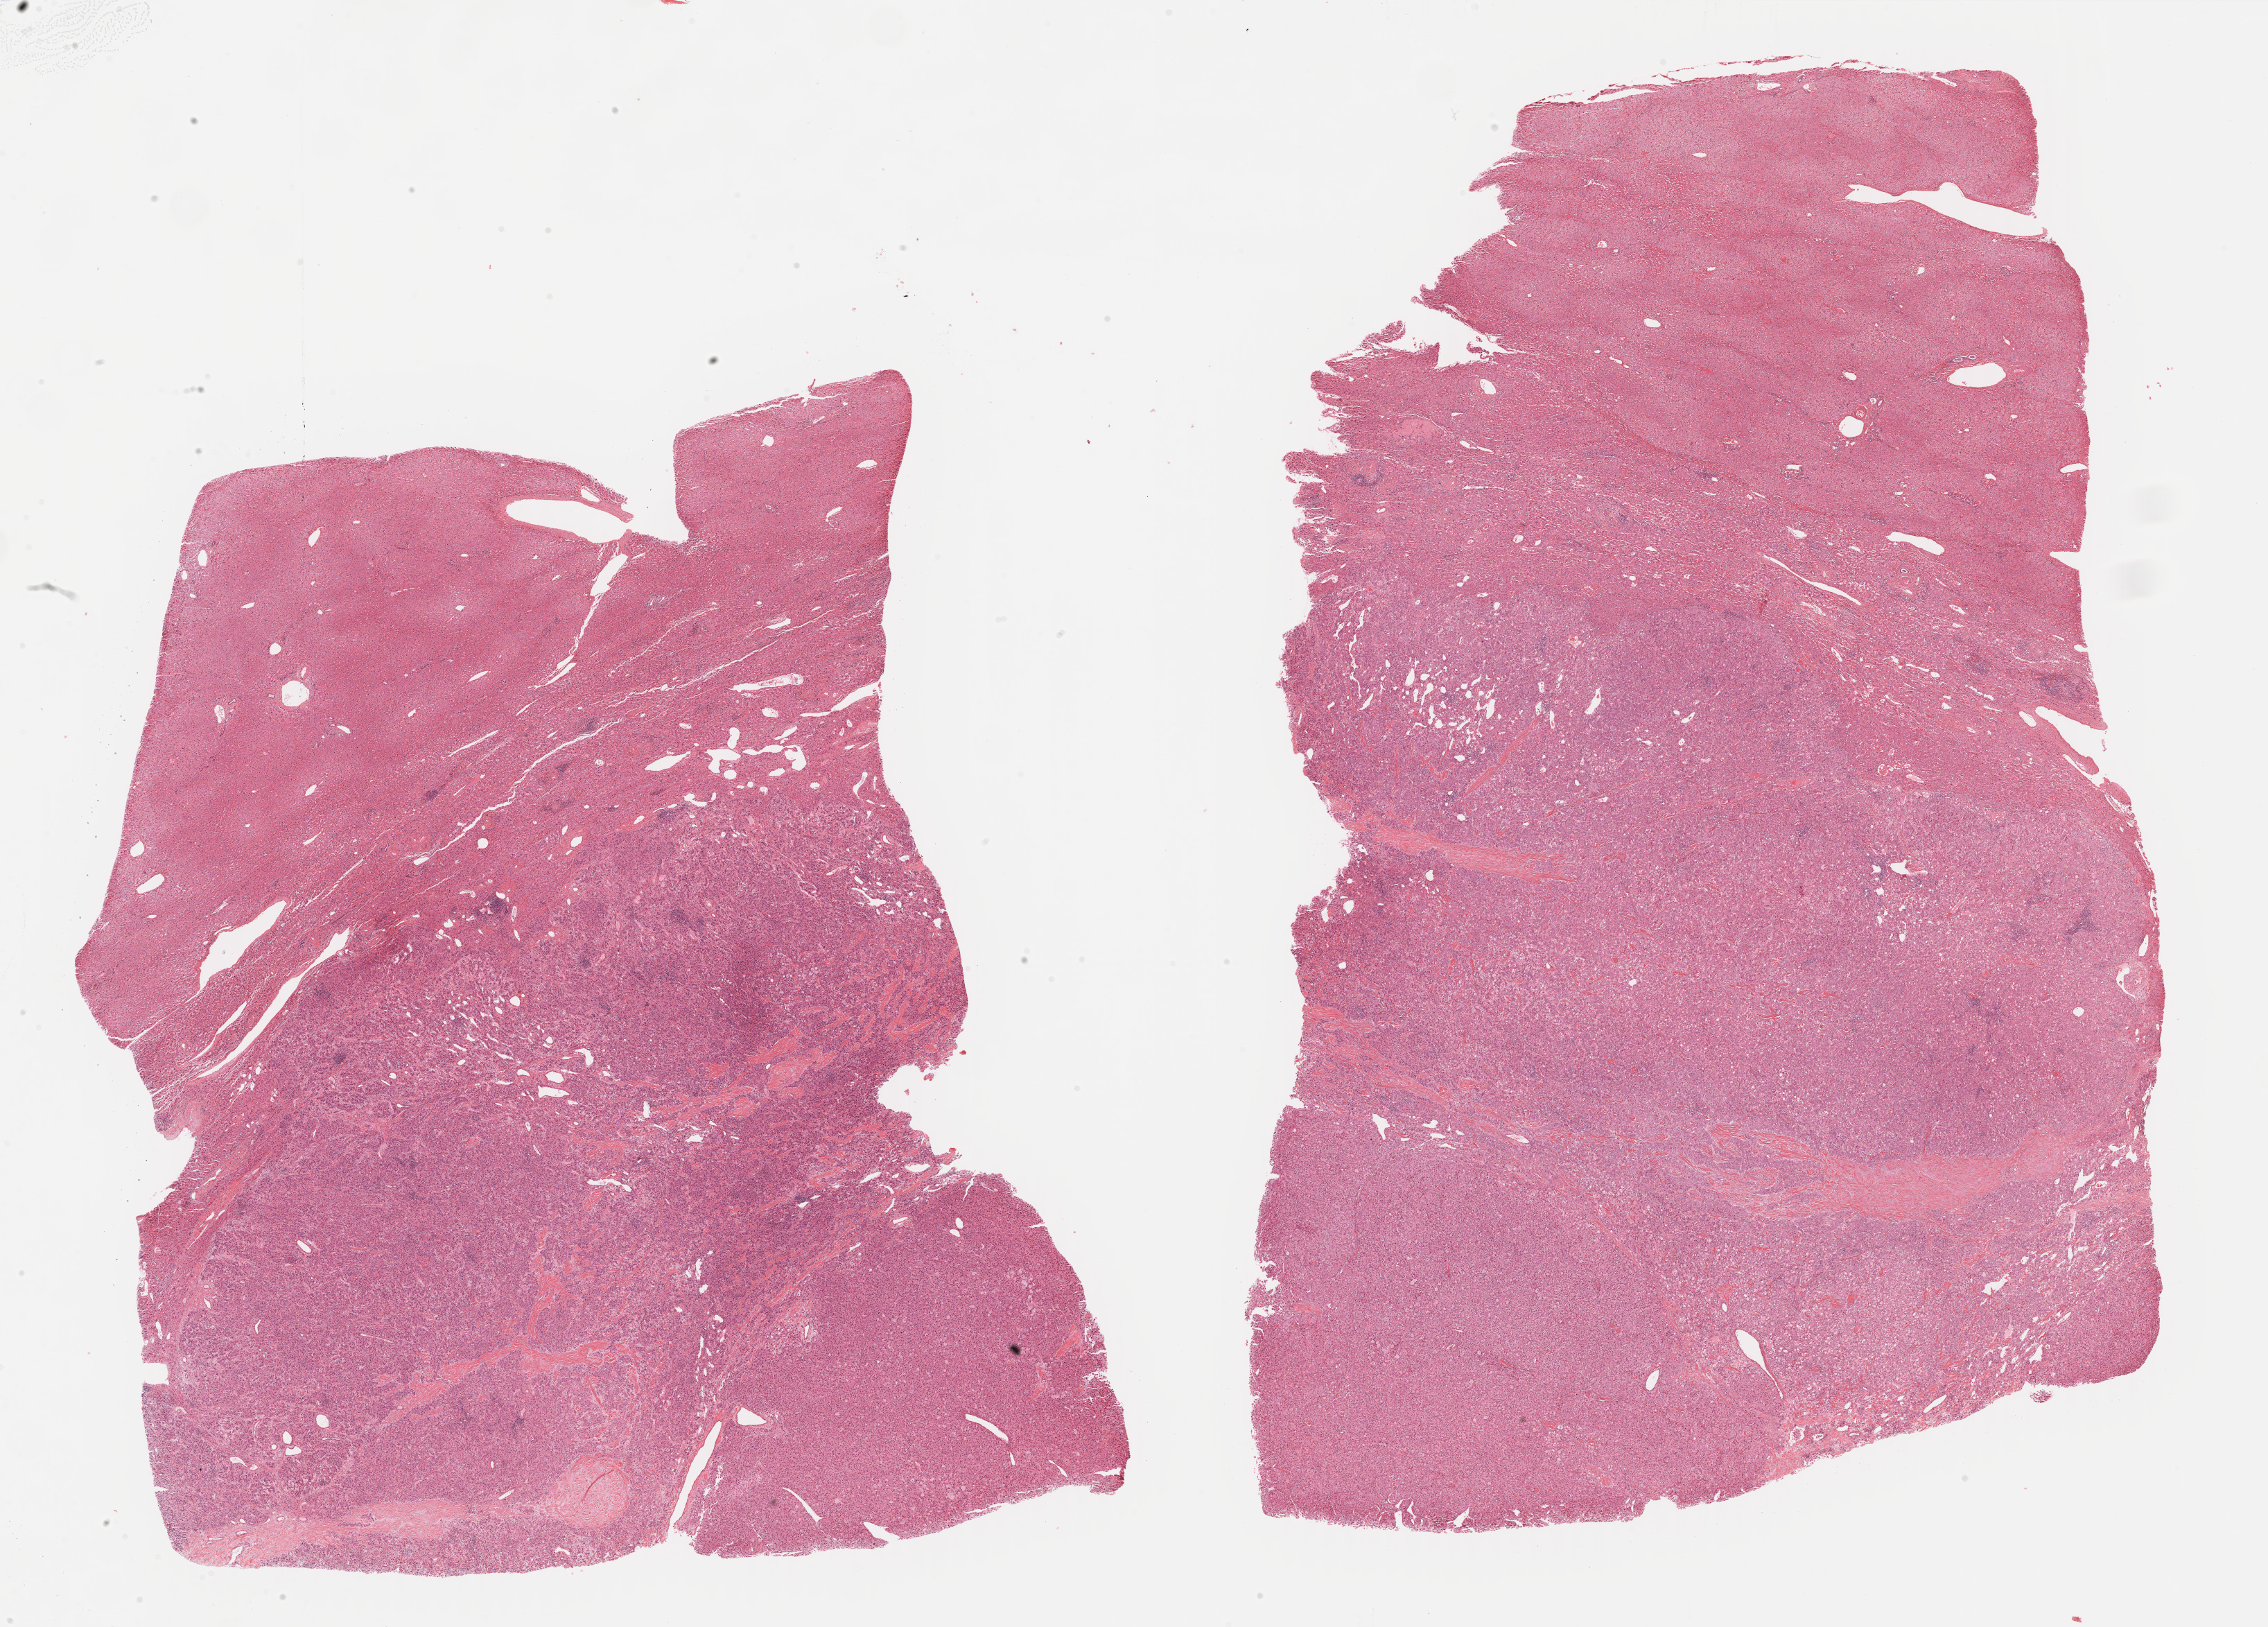
Whole-slide histology image, Hematoxylin and eosin (H&E) stained, shown as a low-resolution overview of the whole scanned area (about 26.5 x 19.0 mm, slide scanned at 40x), FFPE section, primary tumour sample from the liver. Patient: female, age at initial diagnosis 77 years. Histologic grade: G2 (moderately differentiated).
Histologic diagnosis: Hepatocellular carcinoma, NOS. AJCC pathologic stage: II (6th edition).